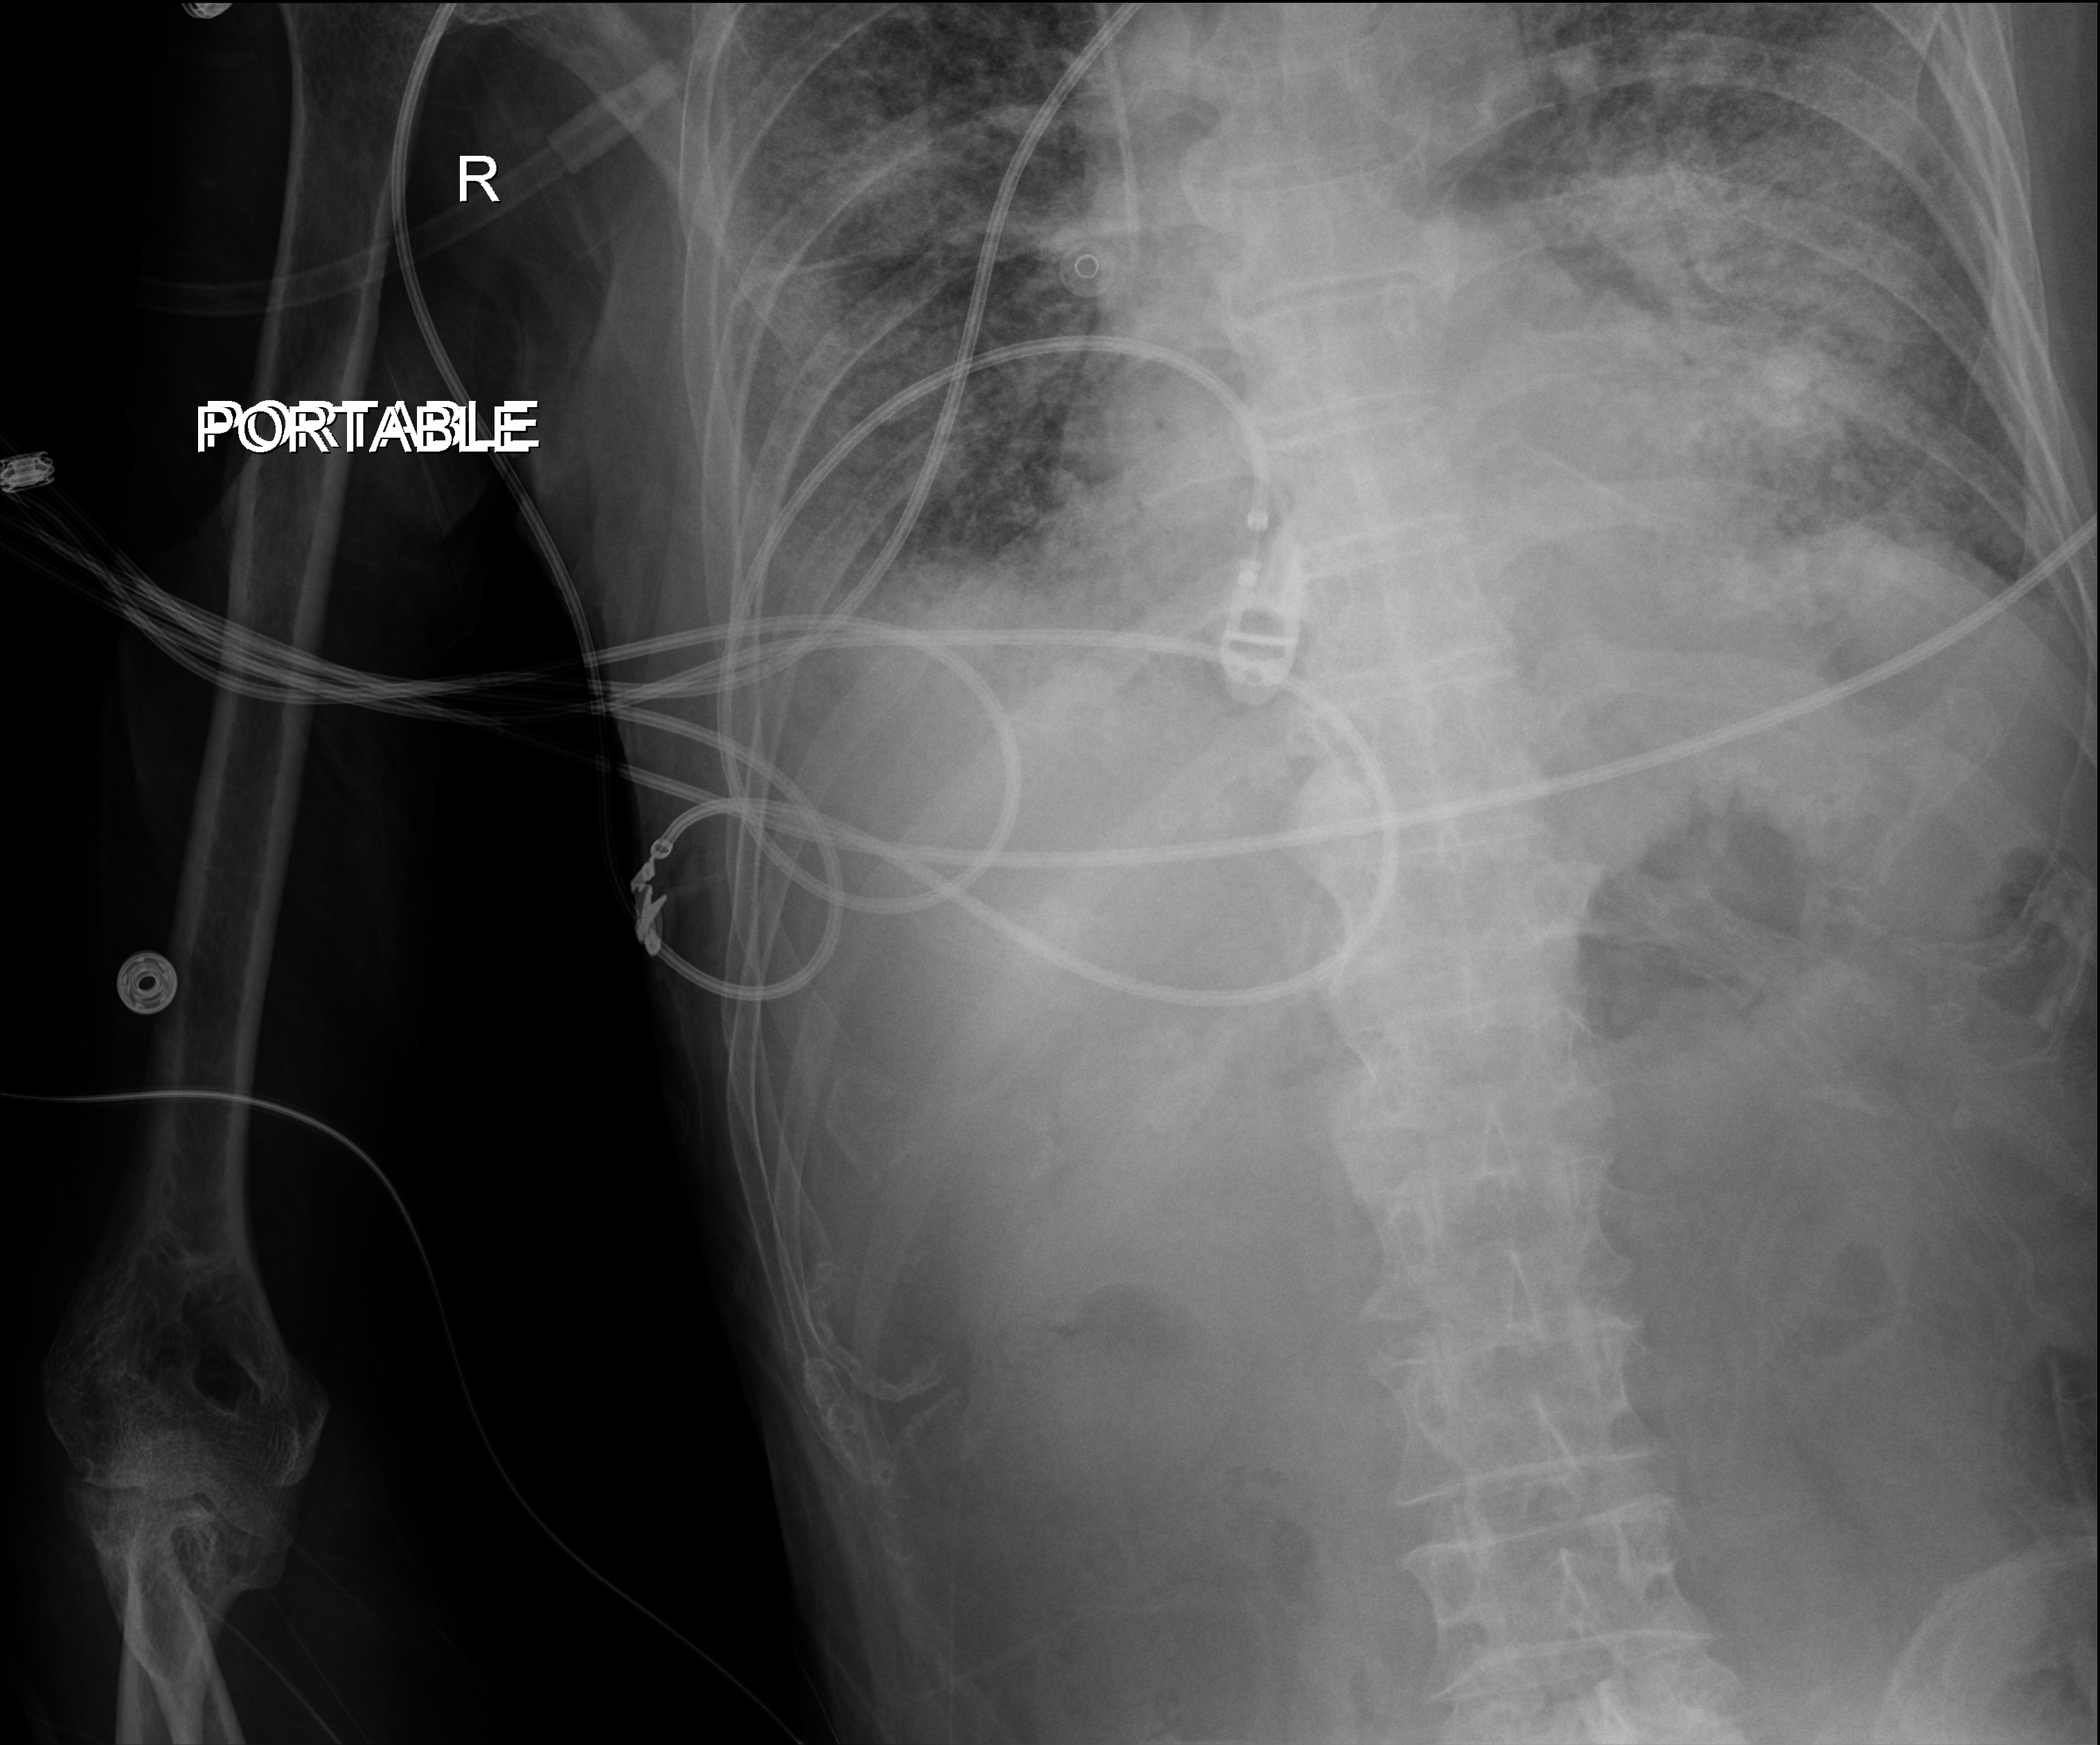
Chest X-ray (portable), anteroposterior (AP) projection. Male patient hospitalised with COVID-19, age 60–74 years.
Hospital-stay facts (about this admission, not read from this image; timing relative to this image not recorded): admitted to intensive care during this hospital stay: yes; mechanically ventilated during this hospital stay: yes; hypertension (admission record): yes.